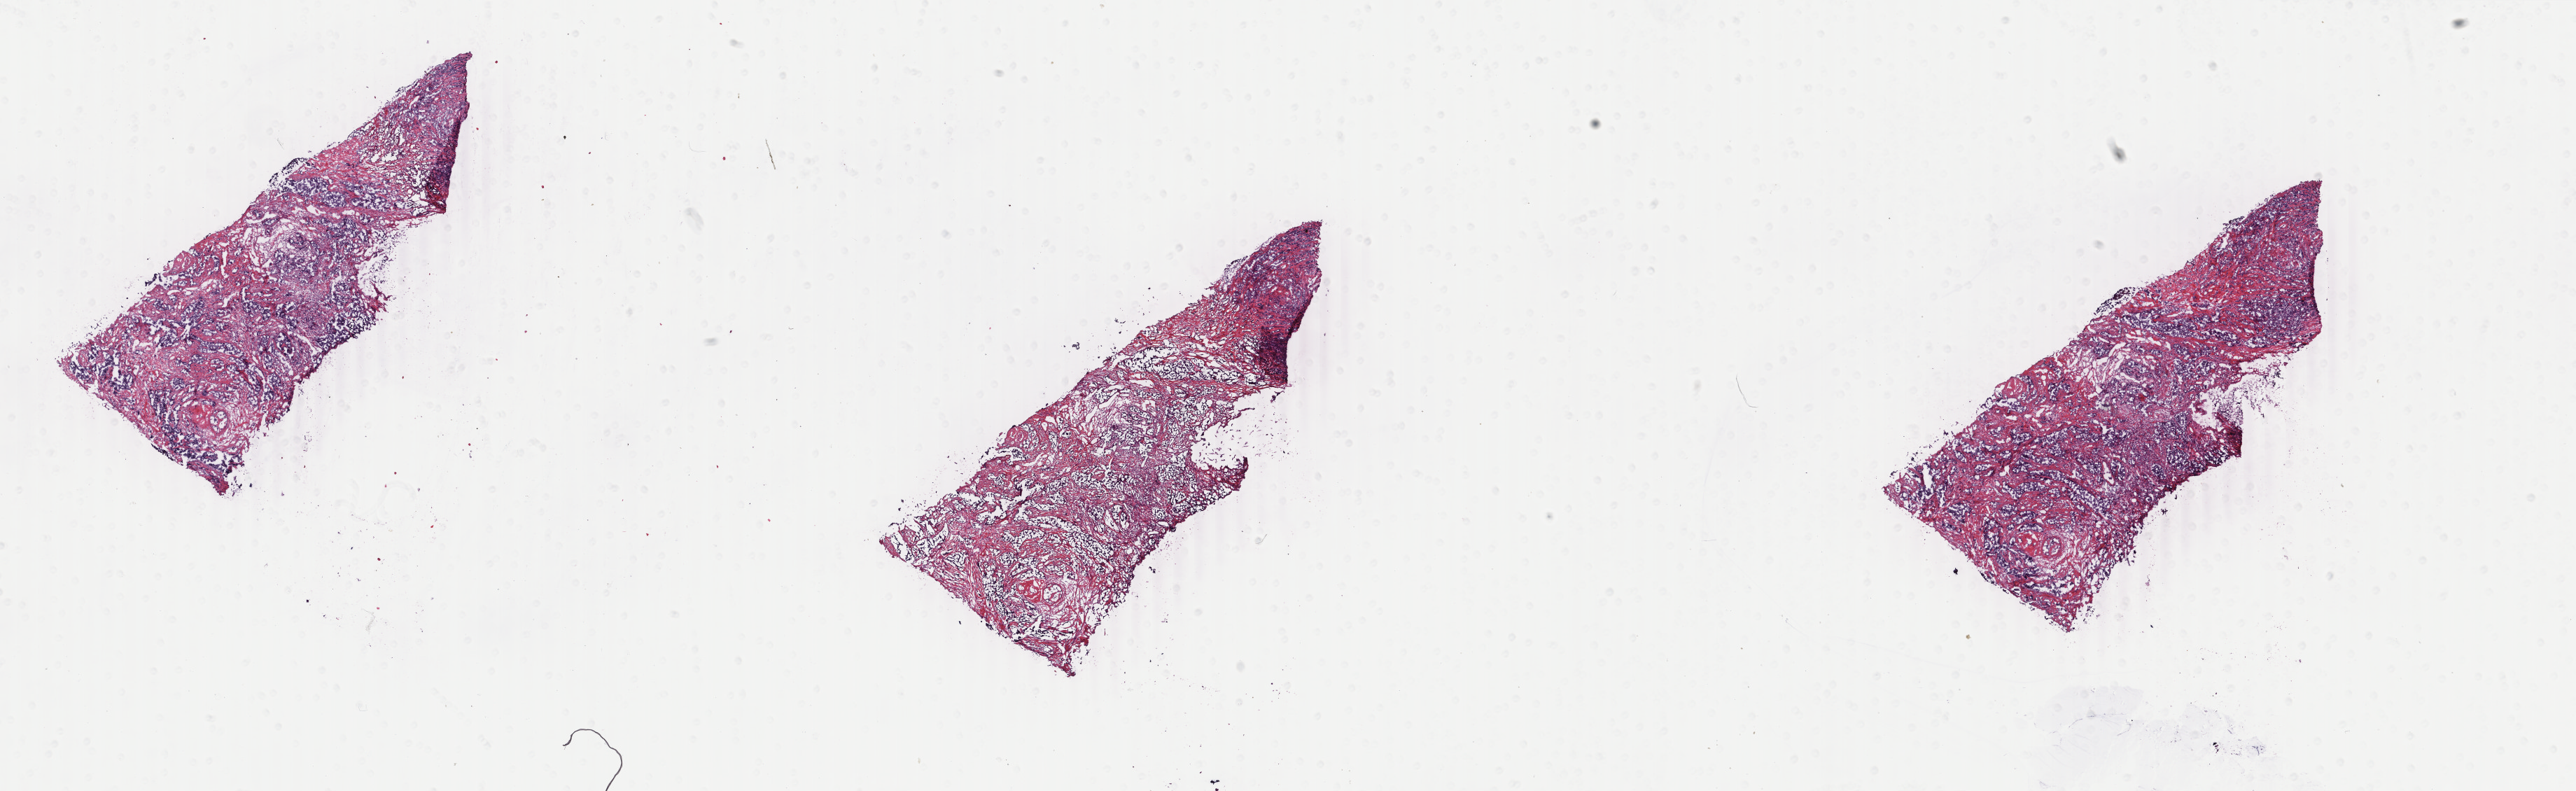
H&E-stained whole-slide image — a low-resolution overview of the entire scanned area, about 29.3 x 9.0 mm (from a 40x scan), frozen section from the bottom of the tissue portion, breast, primary tumour sample. Patient: female, age at initial diagnosis 49 years. Slide review estimates, as recorded: tumour cells 85%, tumour nuclei 85%, normal cells 0%, stromal cells 15%, necrosis 0%. Infiltration values recorded for this section: lymphocyte infiltration 2%, monocyte infiltration 0%, neutrophil infiltration 0%.
Pathologic diagnosis: Infiltrating duct carcinoma, NOS. TNM: T1c N1 M0. AJCC pathologic stage: IIA (3rd edition). Laterality: left. Lymph nodes positive (case pathology): 6 of 32 examined.